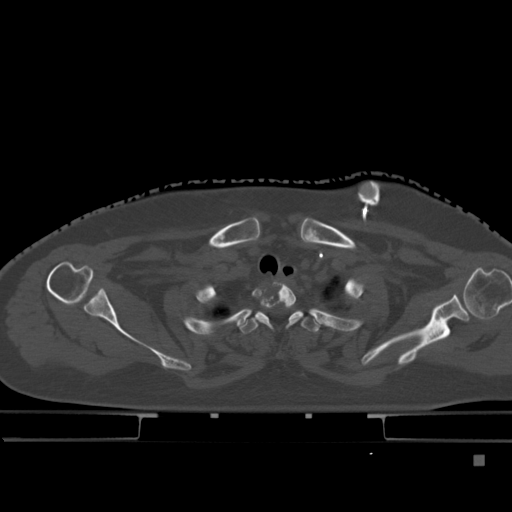
CT including the spine, one axial slice. Position 365 of 495 along the scan axis. Bone window (W 1800 / L 400 HU). 1.5 mm slice thickness. 512 × 512 image matrix, field of view 404 × 404 mm. Female patient, age 33 years. Case-level facts recorded for this patient, not image findings: primary cancer: breast.
Structures marked on this image (semi-automatic segmentation, software-assisted and operator-edited):
- T1 vertebra: bounding box <260,282,300,327> (left, top, right, bottom; pixels)
- T2 vertebra: <238,310,342,334>